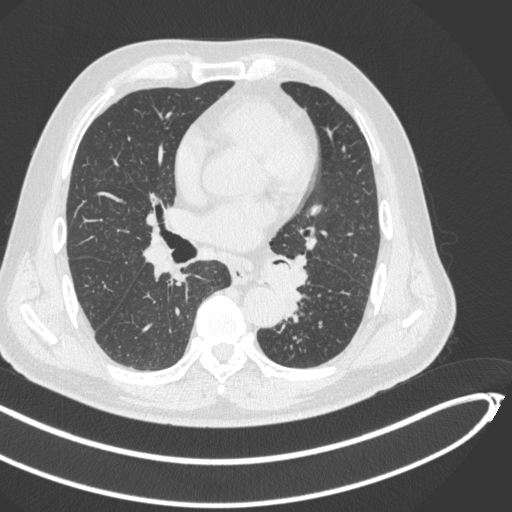
Chest CT, one axial slice. Slice 242 of 466 in the series (ordered by position). 120 kVp. Lung window (W 1500 / L -600 HU). 512 × 512 image matrix, field of view 400 × 400 mm. Patient: male, 64 years. From the clinical record (not read from this slice): clinical TNM (as recorded): T1c N0 M0.
Structures marked on this image (bounding box drawn by a radiologist):
- lung tumour (recorded histology: squamous cell carcinoma): bounding box [x1, y1, x2, y2] px = [259, 258, 301, 309]